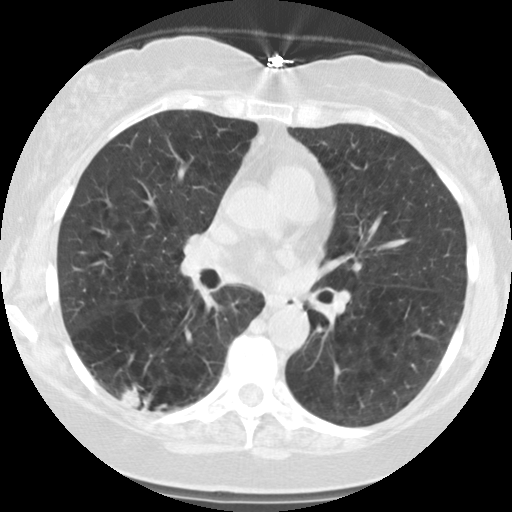
Low-dose screening chest CT, one axial slice; position 61 of 122 along the scan axis; 140 kVp; lung window (W 1500 / L -600 HU); 512 × 512 image matrix.
Structures marked on this image (manually delineated by an expert):
- lesion 1 (tumor, lower lobe of right lung): bounding box <121,385,140,408> (left, top, right, bottom; pixels)